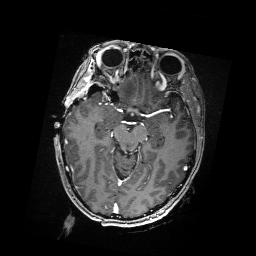
Brain MRI from a brain-tumour surgery series, one axial slice; position 107 of 176 along the scan axis; T1-weighted post-contrast; 256 × 256 image matrix, field of view 256 × 256 mm. From the clinical record (not read from this slice): histopathology: Metastatic Carcinoma from Breast primary; tumour location: Right Frontal.
Outlined on this slice (manually delineated by an expert):
- residual tumour: bounding box <89,86,97,96> (left, top, right, bottom; pixels)